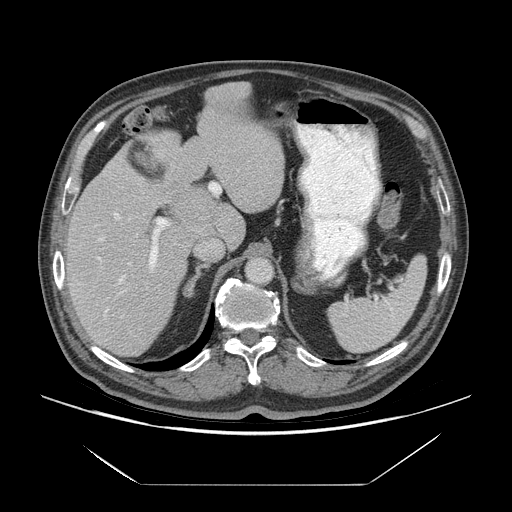
Contrast-enhanced abdominal CT (liver protocol), one axial slice; position 43 of 75 along the scan axis; soft-tissue window (W 400 / L 40 HU); 2.5 mm slice thickness; 512 × 512 image matrix, field of view 420 × 420 mm. Case-level facts recorded for this patient, not image findings: diagnosis: hepatocellular carcinoma (patient treated with transarterial chemoembolisation; whether this scan precedes or follows treatment is not stated here); TNM stage (as recorded): Stage-I; Child-Pugh class: A; tumour nodularity: uninodular.
Annotated regions visible in this slice (semi-automatically segmented with operator editing):
- liver parenchyma outside the tumour (the mass and vessels are separate outlines, so this box may not span the whole liver): bounding box [x1, y1, x2, y2] px = [66, 82, 284, 356]
- mass: [173, 186, 213, 223]
- liver vessels: [78, 213, 170, 318]